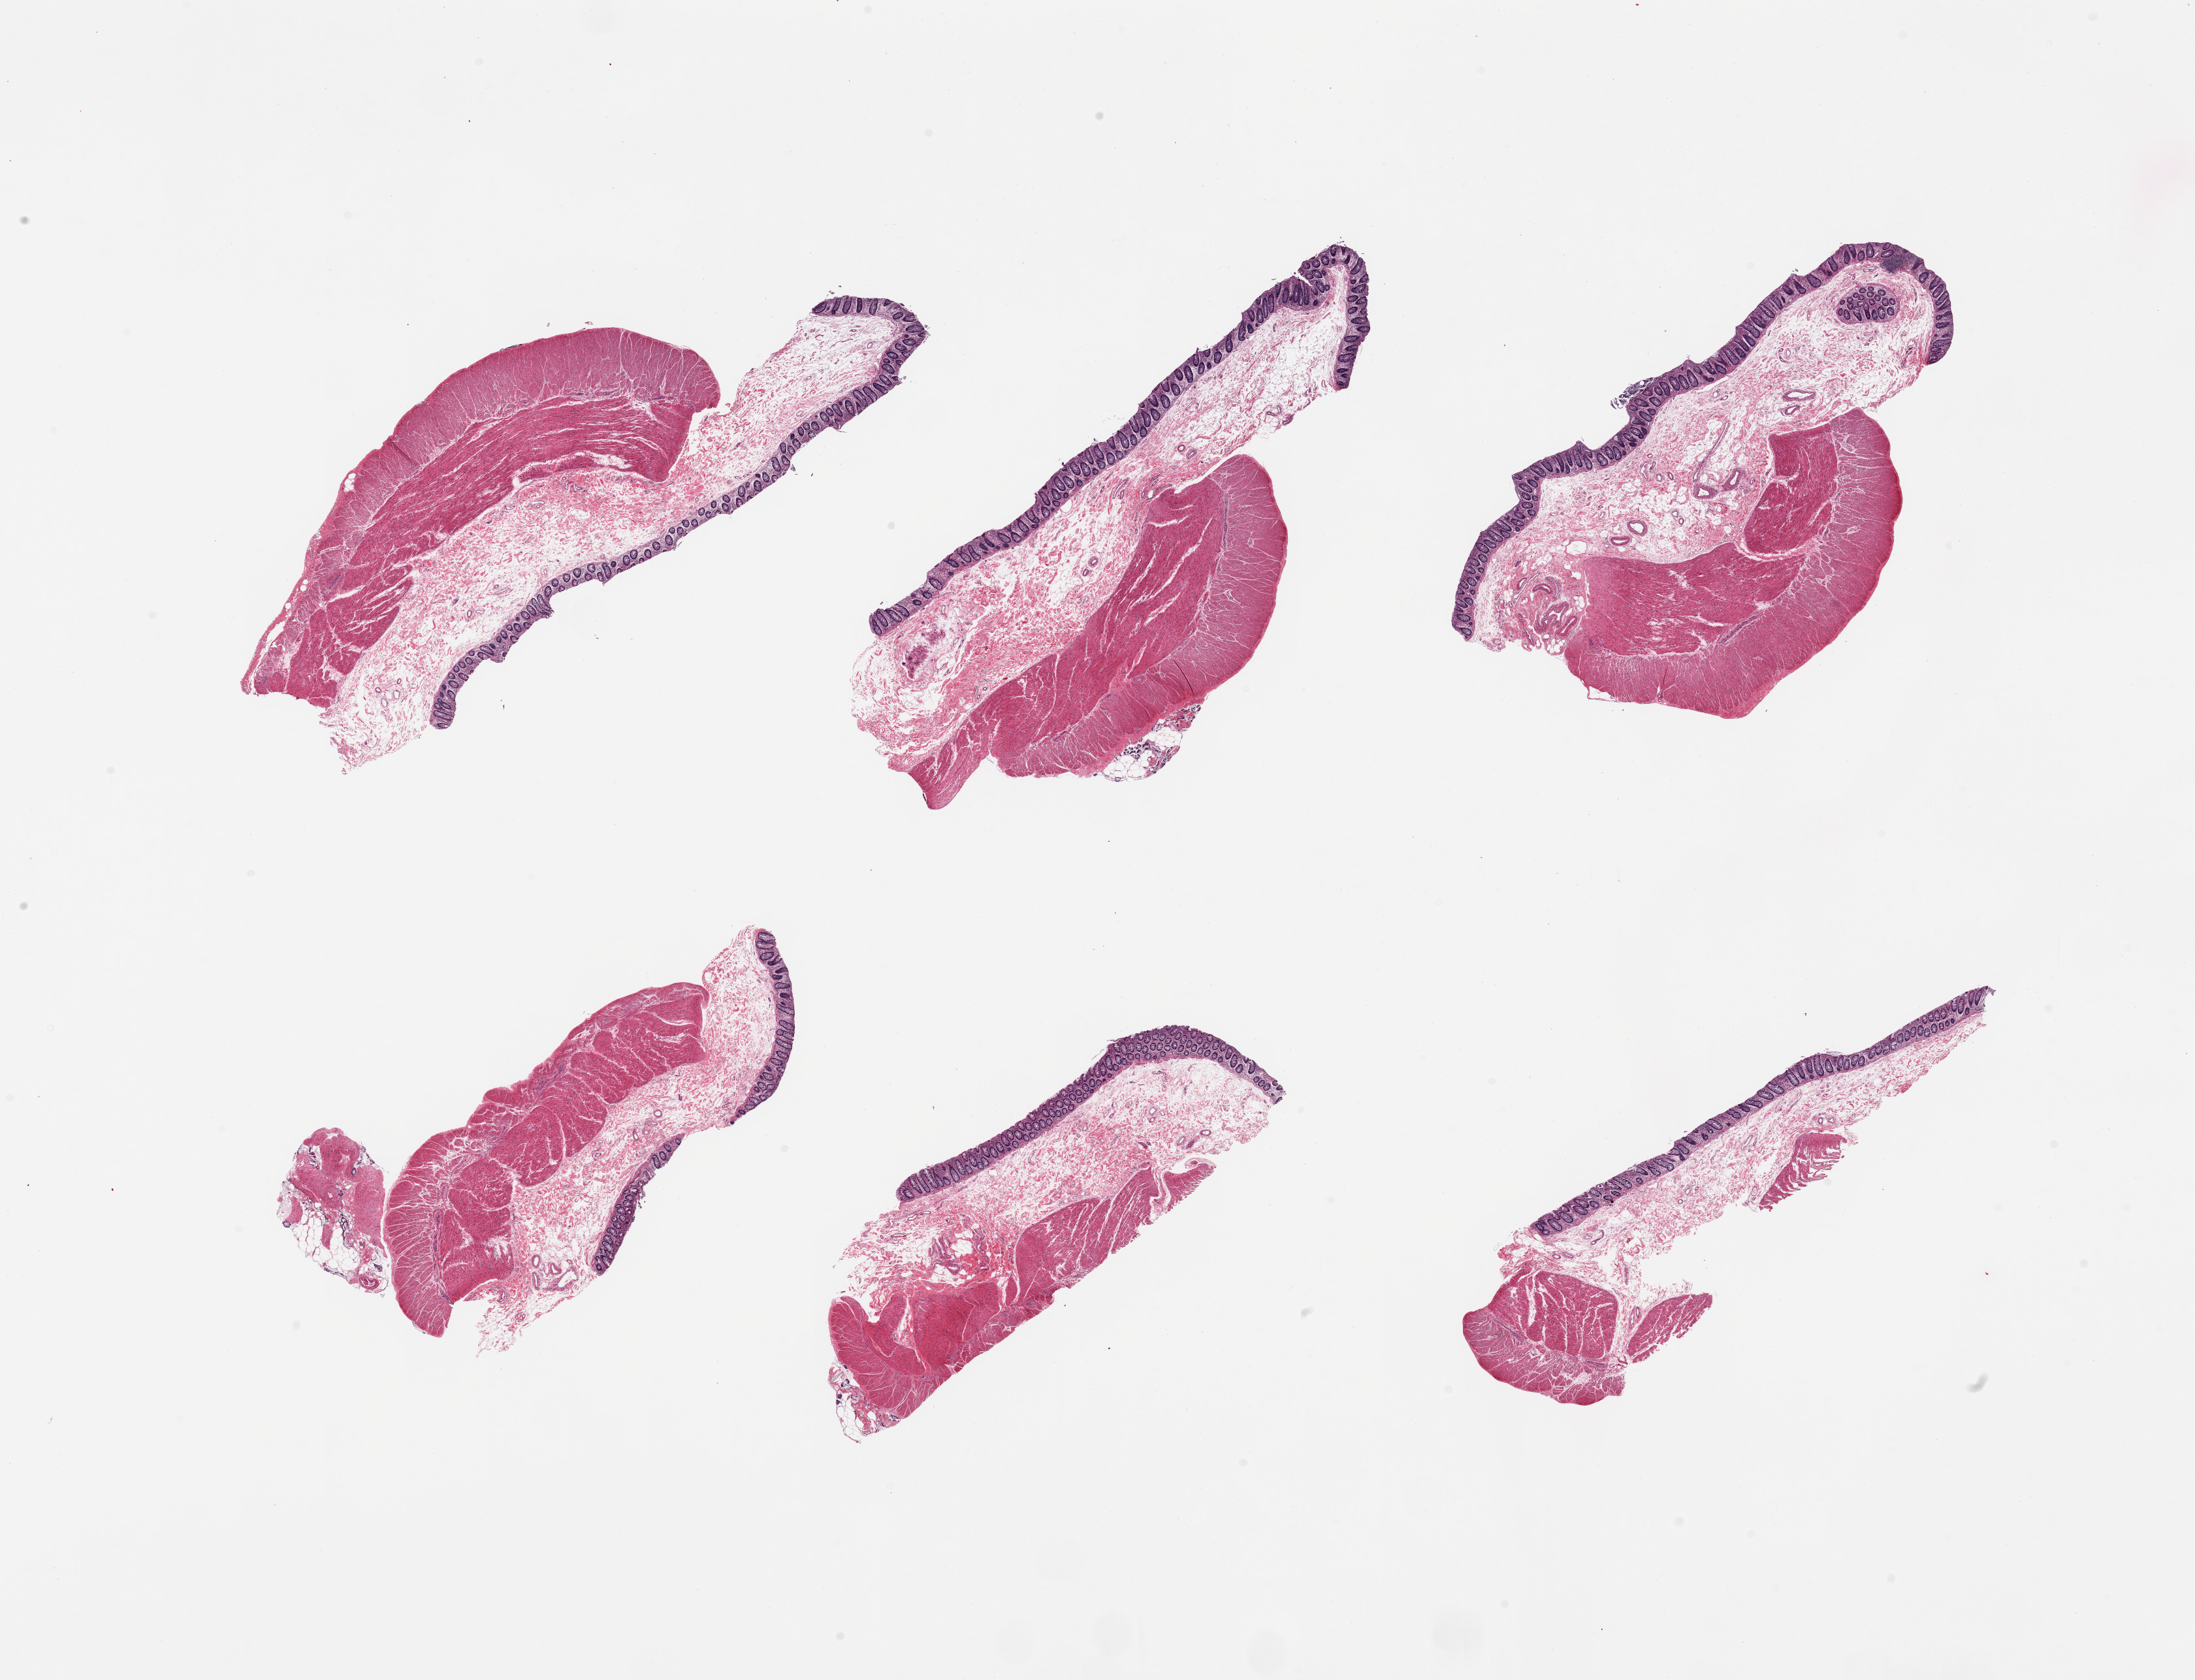
Digitized haematoxylin and eosin-stained section, whole scanned area (about 26.6 x 20.3 mm, slide scanned at 20x) shown as a low-resolution overview. PAXgene-fixed, paraffin-embedded tissue. Target tissue: transverse colon. Donor tissue sample. Female donor.
* review note (as recorded): 6 pieces; all with mucosa/submucosa/muscularis